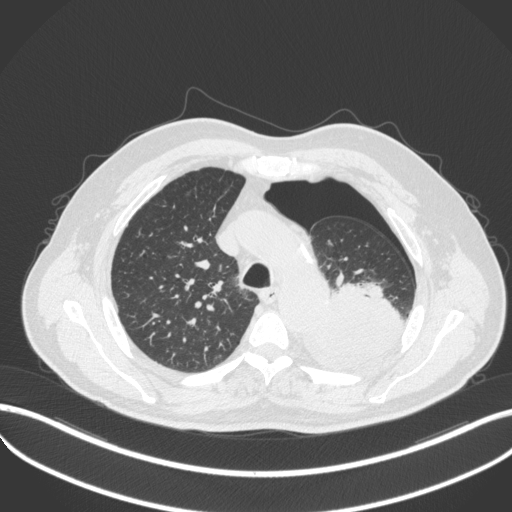
Chest CT, one axial slice. Slice 377 of 466 in the series (ordered by position). Reconstruction kernel B31f. 120 kVp. Lung window (W 1500 / L -600 HU). 512 × 512 image matrix, field of view 400 × 400 mm. Male patient, age 76 years. From the clinical record (not read from this slice): clinical TNM (as recorded): T3 N0 M1b.
Structures marked on this image (bounding box drawn by a radiologist):
- lung tumour (recorded histology: adenocarcinoma): bounding box (x1, y1, x2, y2) in pixels: (299, 276, 405, 370)